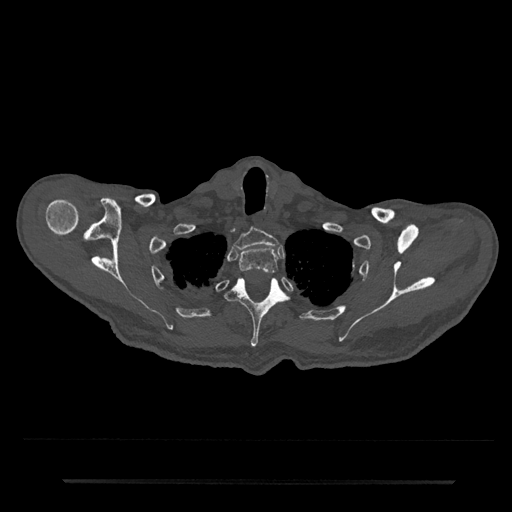
CT including the spine, one axial slice. Position 674 of 797 along the scan axis. Bone window (W 1800 / L 400 HU). 0.5 mm slice thickness. 512 × 512 image matrix. Male patient, age 74 years. From the clinical record (not read from this slice): primary cancer: prostate.
Annotated regions visible in this slice (semi-automatically segmented with operator editing):
- T1 vertebra: box from (x=233, y=228) to (x=279, y=250) px
- T2 vertebra: (x=239, y=247)–(x=278, y=275)
- T3 vertebra: (x=226, y=277)–(x=288, y=347)